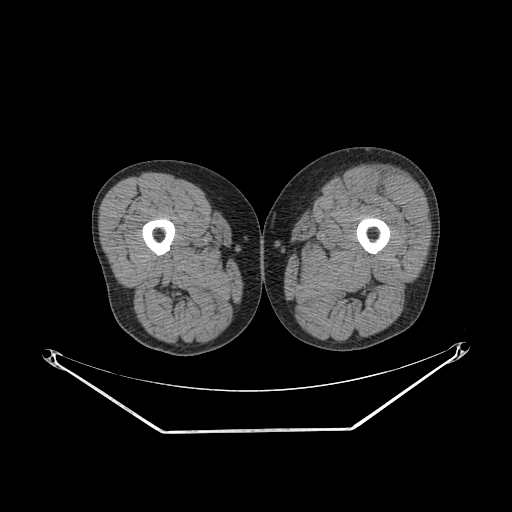
CT of an extremity soft-tissue mass (from a PET/CT study), one axial slice; slice 217 of 267 in the series (ordered by position); reconstruction kernel SOFT; soft-tissue window (W 400 / L 40 HU); 3.75 mm slice thickness; 512 × 512 image matrix, field of view 500 × 500 mm. Male patient. From the clinical record (not read from this slice): histological type: extraskeletal osteosarcoma; grade: high; site of the primary tumour: thigh.
Annotated regions visible in this slice (expert contour drawn on MRI and transferred to this co-registered scan by the dataset authors):
- gross tumour volume (mass): box from (x=384, y=178) to (x=398, y=202) px